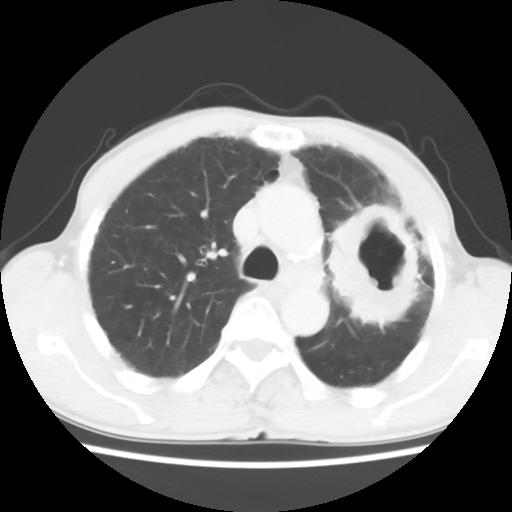
Chest CT, one axial slice. Slice 42 of 60 in the series (ordered by position). Reconstruction kernel STANDARD. Lung window (W 1500 / L -600 HU). 5 mm slice thickness. 512 × 512 image matrix. Male patient, age 64 years. Case-level facts recorded for this patient, not image findings: clinical TNM (as recorded): T3 N3 M0.
Structures marked on this image (bounding box drawn by a radiologist):
- lung tumour (recorded histology: adenocarcinoma): bounding box <316,191,437,346> (left, top, right, bottom; pixels)